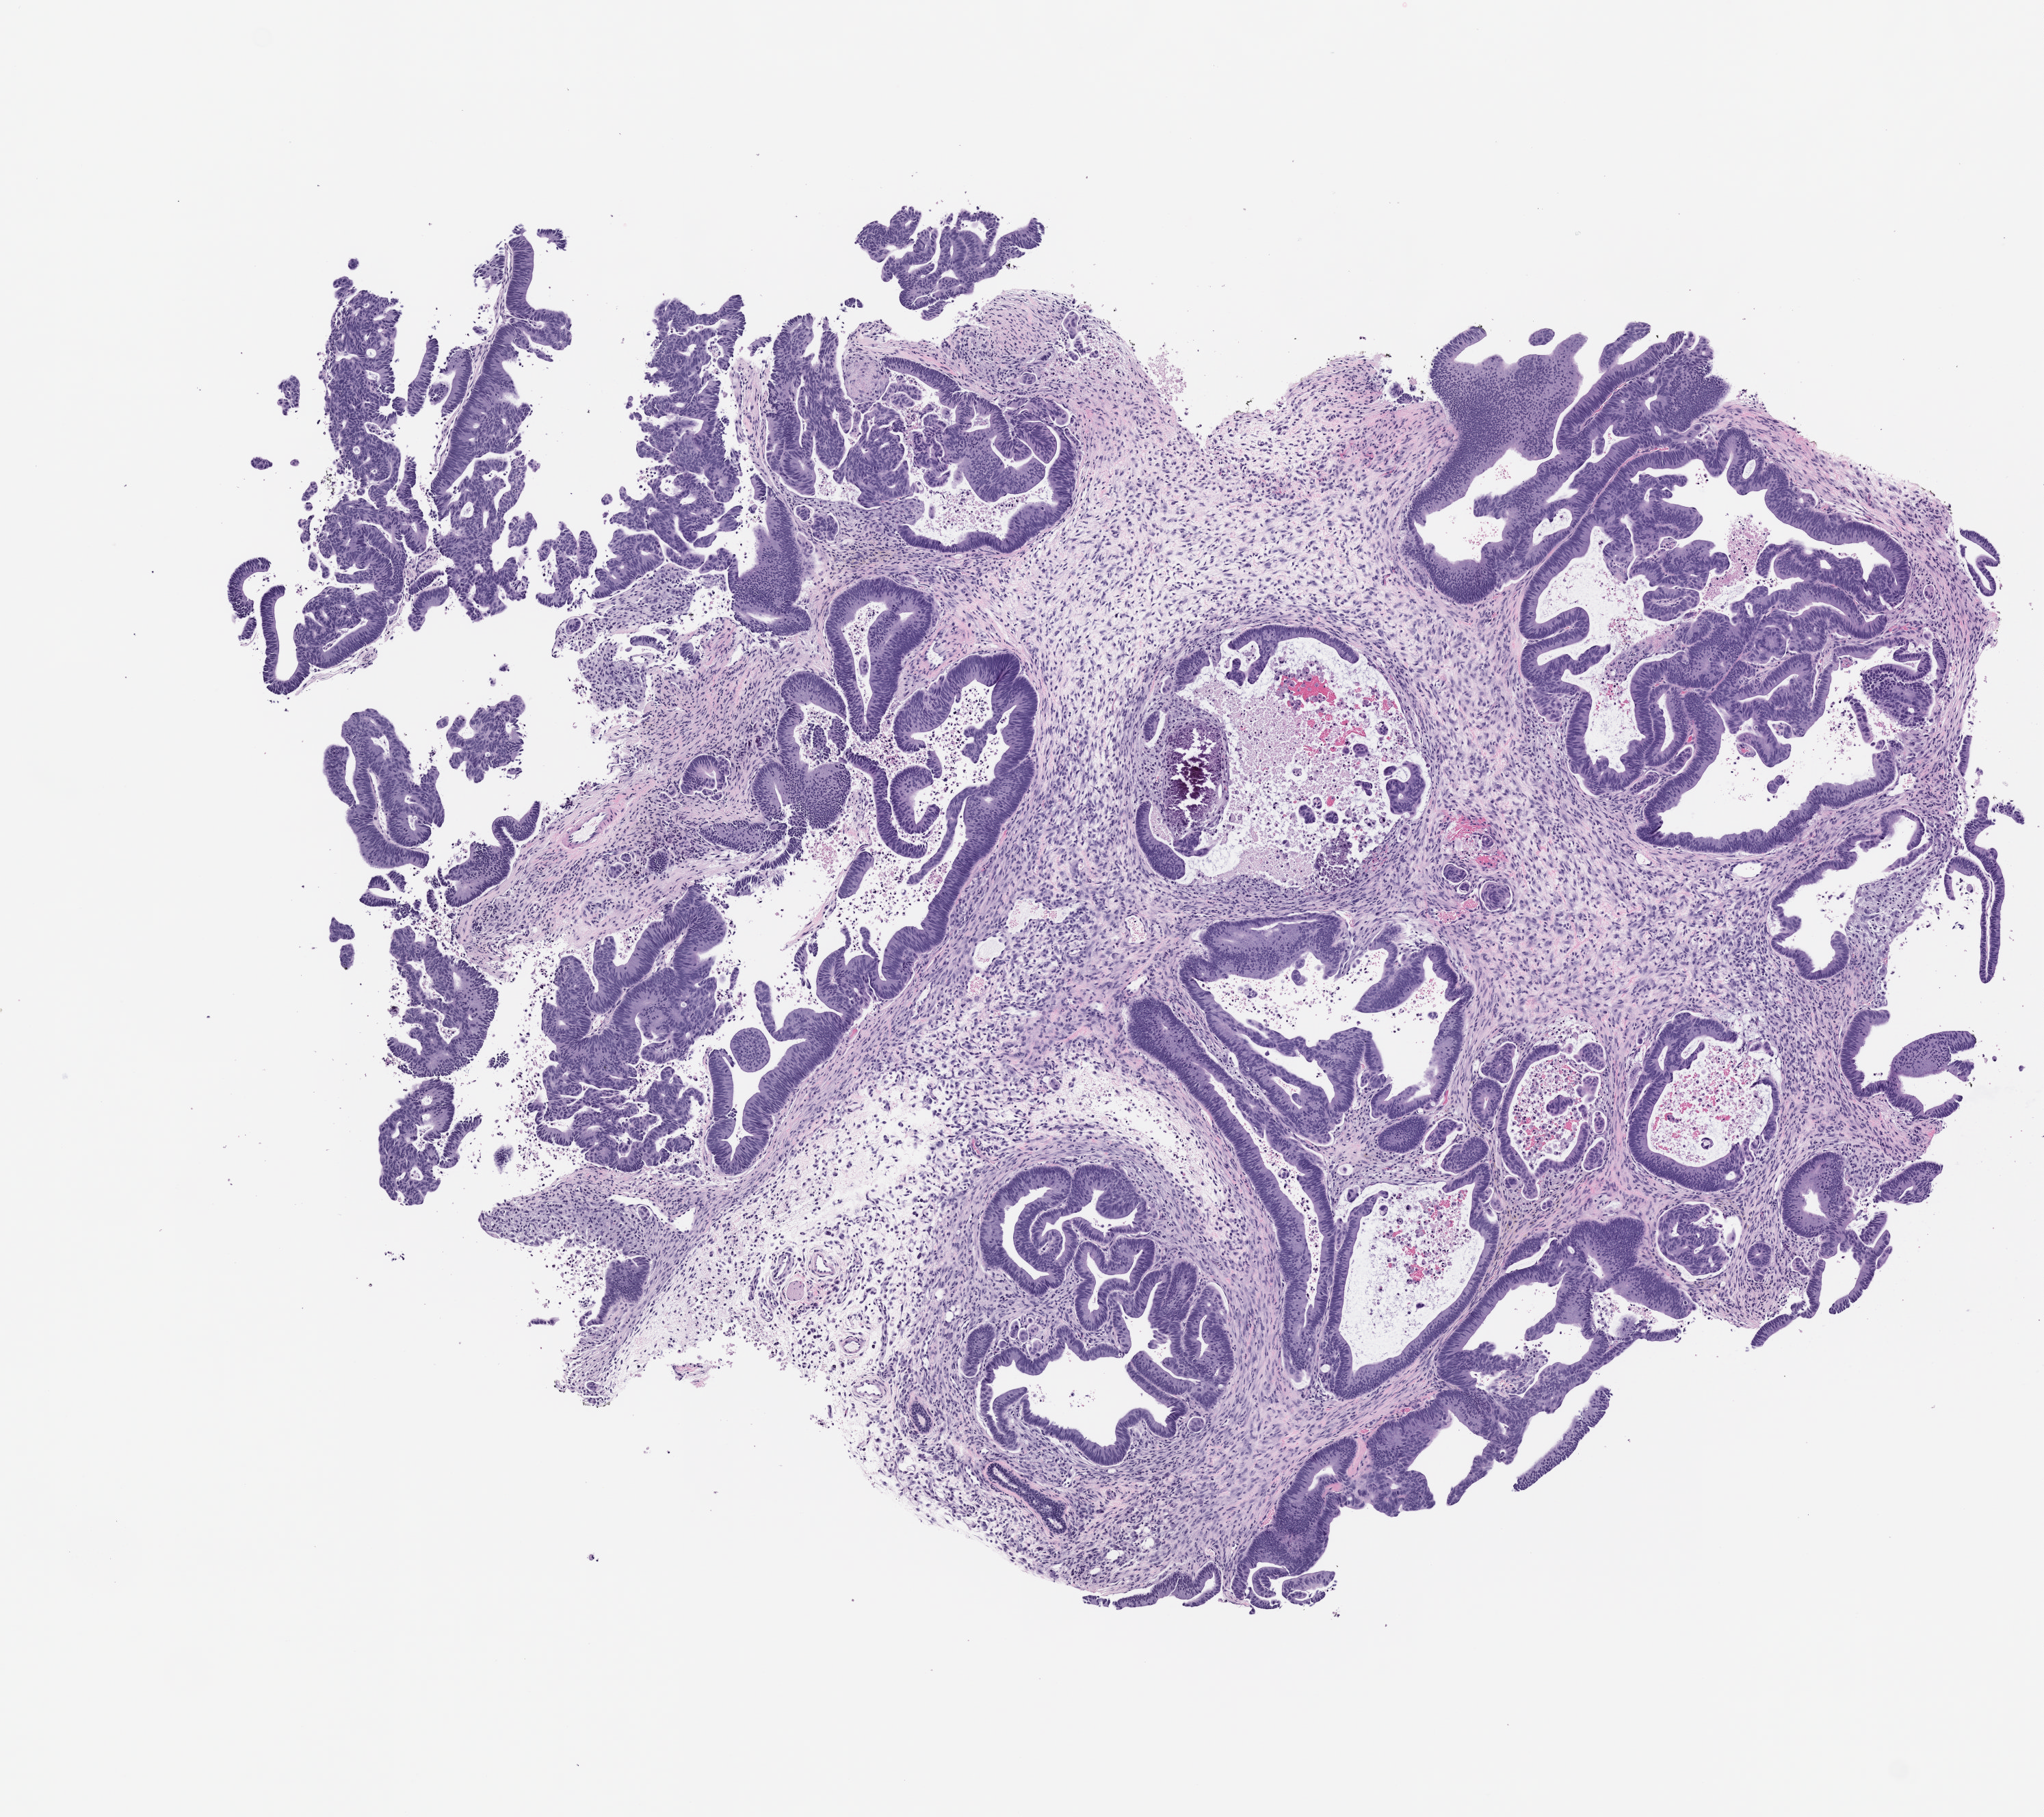
Whole-slide image, H&E: patient-derived xenograft (human tumor grown in a mouse), passage 2 — a low-resolution overview of the entire scanned area, about 6.0 x 5.3 mm; formalin-fixed paraffin-embedded section; originating tumor site category: gastrointestinal tract.
Originating patient diagnosis: Colorectal Carcinoma.